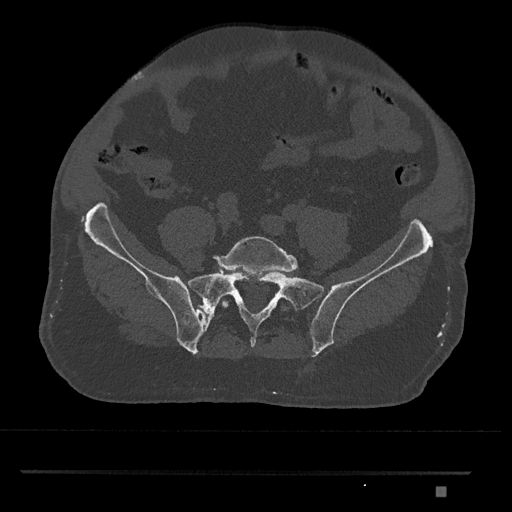
CT including the spine, one axial slice; position 522 of 1134 along the scan axis; reconstruction kernel Br40s/3; bone window (W 1800 / L 400 HU); 512 × 512 image matrix, field of view 429 × 429 mm. Patient: male, 65 years. From the clinical record (not read from this slice): primary cancer: prostate.
Structures marked on this image (semi-automatic segmentation, software-assisted and operator-edited):
- L5 vertebra: bounding box [x1, y1, x2, y2] px = [214, 236, 298, 308]